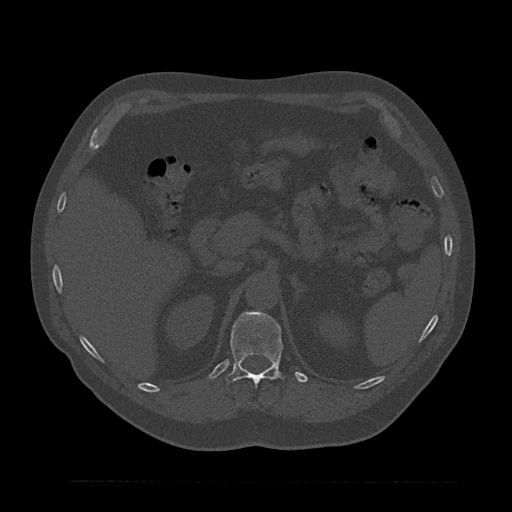
CT including the spine, one axial slice. Slice 228 of 797 in the series (ordered by position). Reconstruction kernel Br40s/3. Bone window (W 1800 / L 400 HU). 512 × 512 image matrix, field of view 430 × 430 mm. Male patient, age 61 years. Case-level facts recorded for this patient, not image findings: primary cancer: prostate.
Structures marked on this image (semi-automatic segmentation, software-assisted and operator-edited):
- T12 vertebra: bounding box <226,312,285,384> (left, top, right, bottom; pixels)